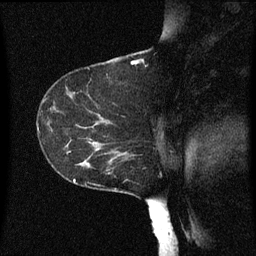
Breast MRI (dynamic contrast-enhanced), one sagittal slice. Position 40 of 60 along the scan axis. Dynamic contrast-enhanced series, image 2 of 3 at this slice position (ordered by acquisition). 1.5 T. TE 4.2 ms, TR 8 ms. 256 × 256 image matrix, field of view 200 × 200 mm. Female patient, age 55 years.
Annotated regions visible in this slice (semi-automatically segmented with operator editing):
- analysis volume of interest (the breast-tissue region the enhancement analysis was run in; not a lesion): bounding box [x1, y1, x2, y2] px = [46, 124, 149, 175]
- tumour enhancement mask (voxels above the 70 % enhancement threshold inside the analysis volume of interest): [70, 140, 127, 159]